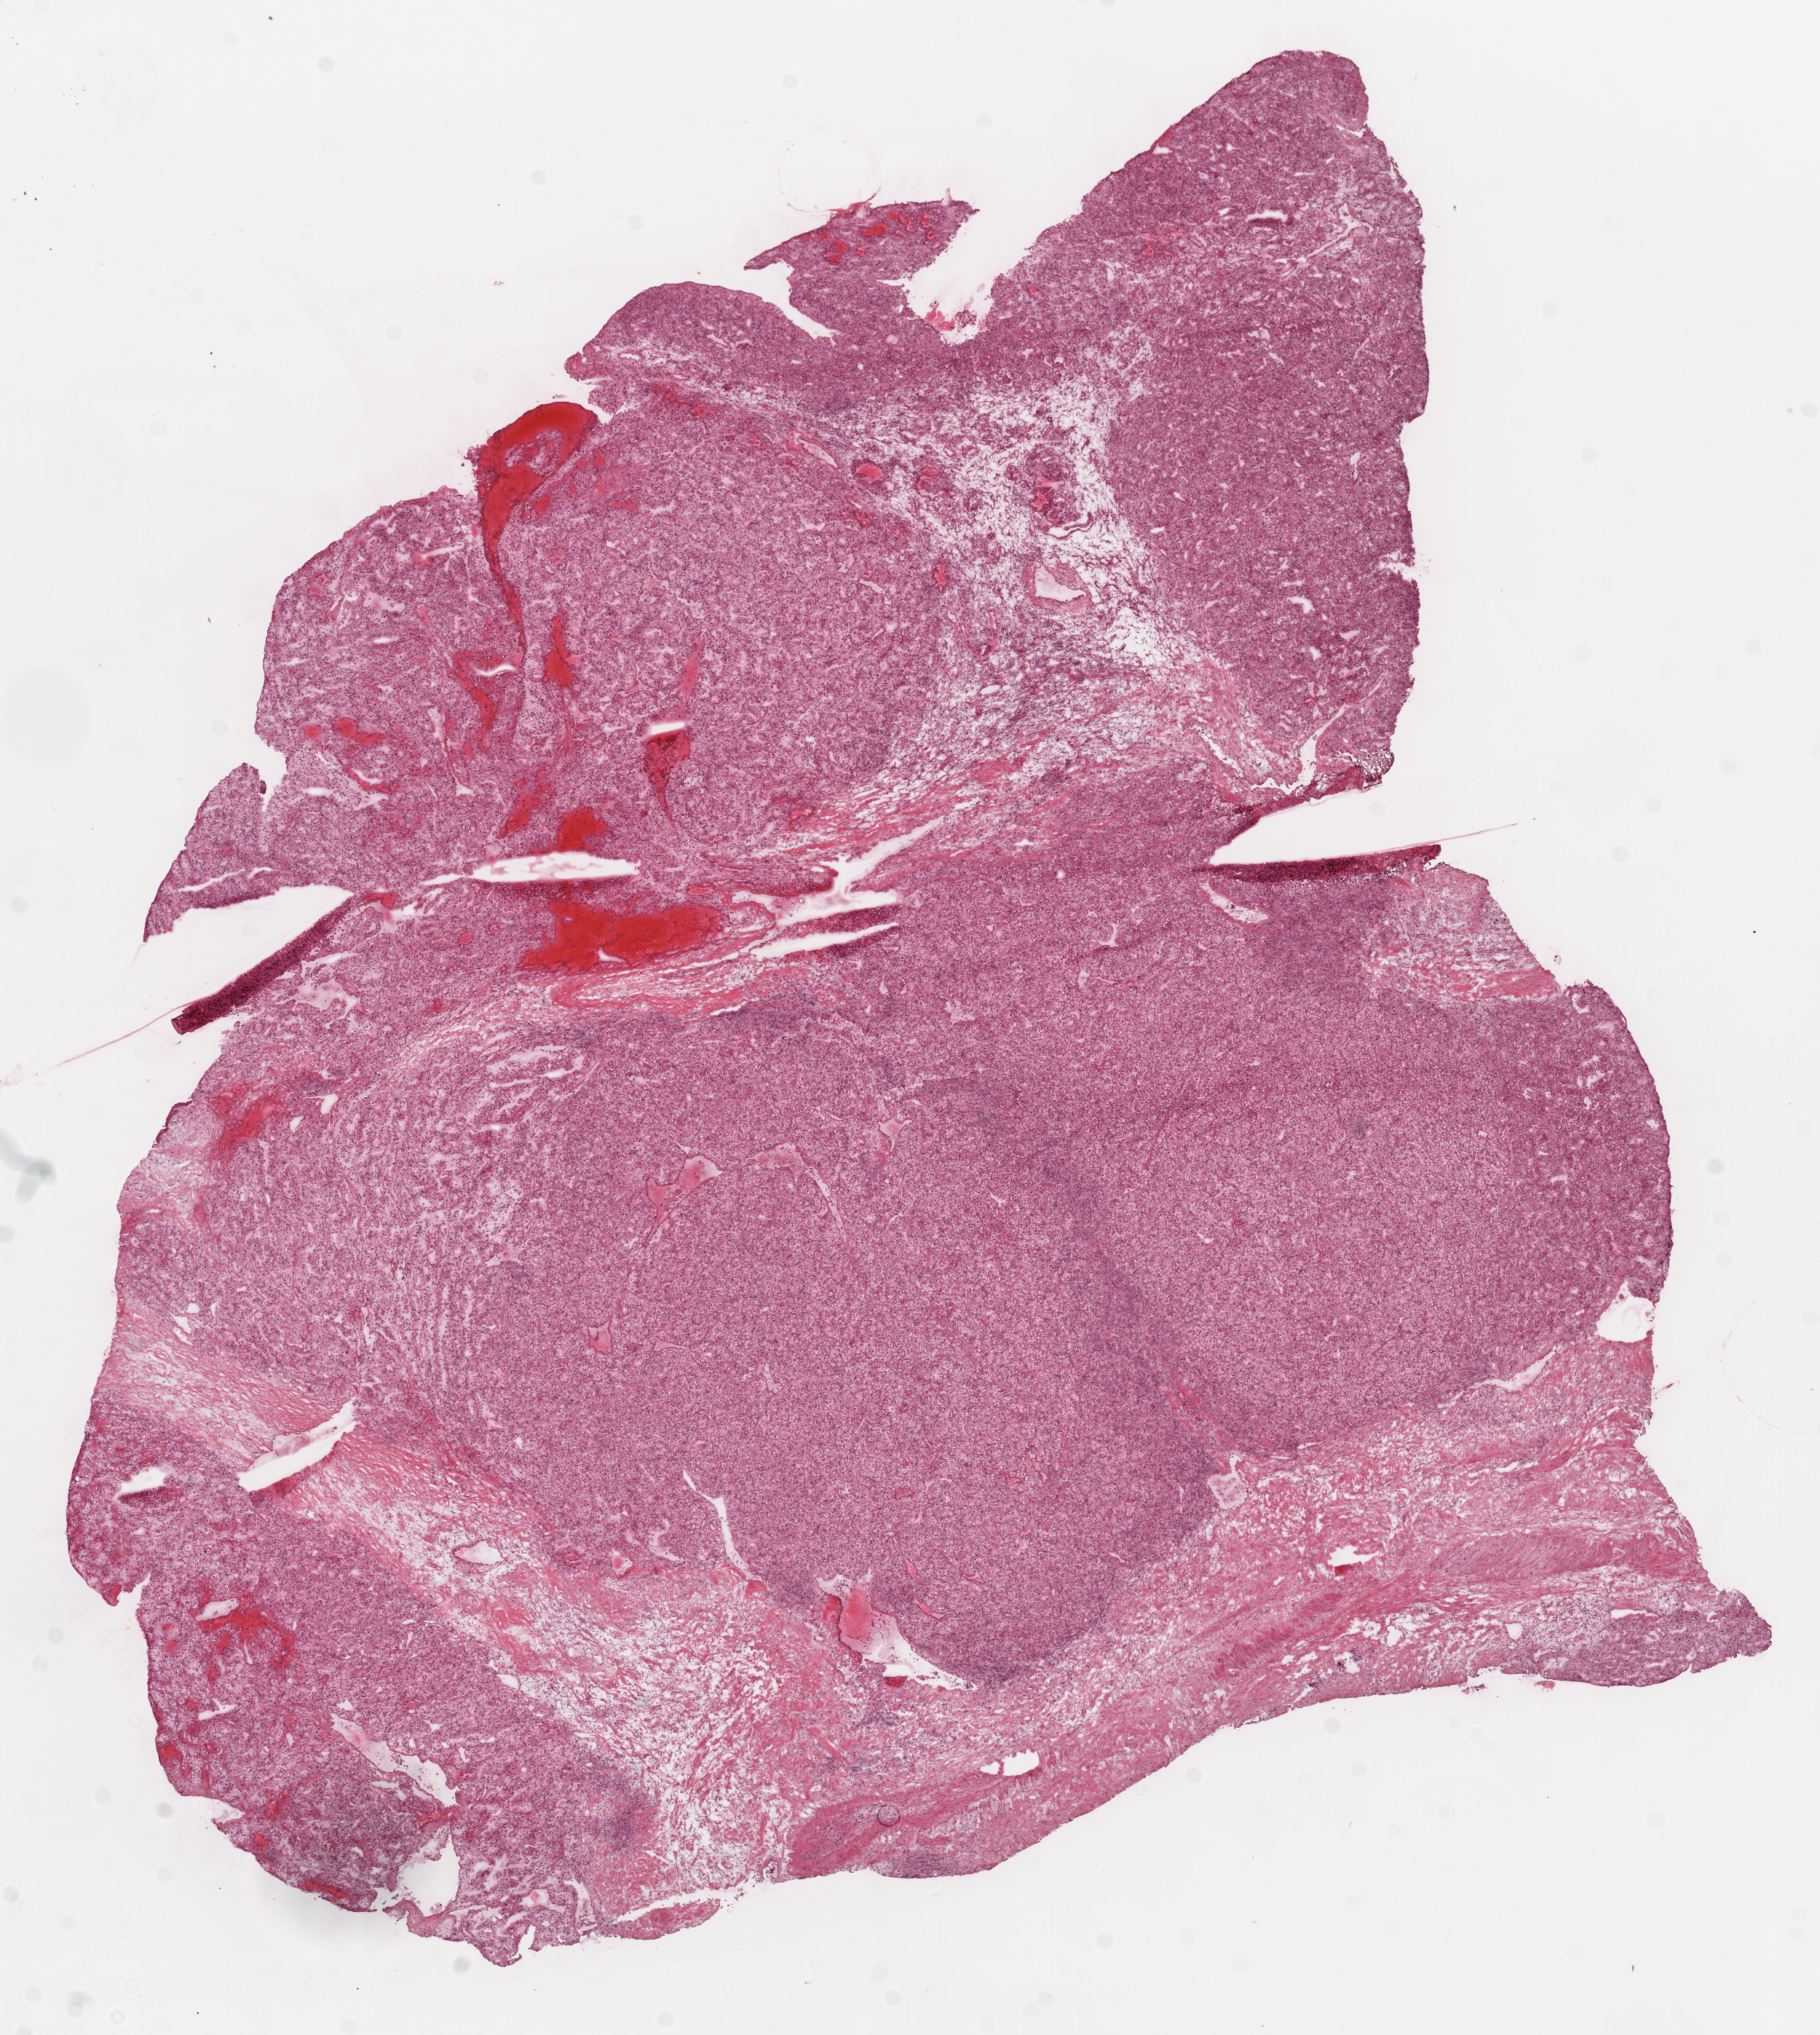
Digitized H&E-stained tissue section (whole slide) — a low-resolution overview of the entire scanned area, about 10.0 x 11.2 mm (slide scanned at 20x). Frozen section from the top of the tissue portion. Primary tumour sample from the kidney. Patient: male, age at initial diagnosis 40 years. Histologic grade: G3 (poorly differentiated). Composition of this section per pathologist review: tumour nuclei 85%, necrosis 0%.
AJCC pathologic stage: I. Laterality: left. Diagnosis: Clear cell adenocarcinoma, NOS.